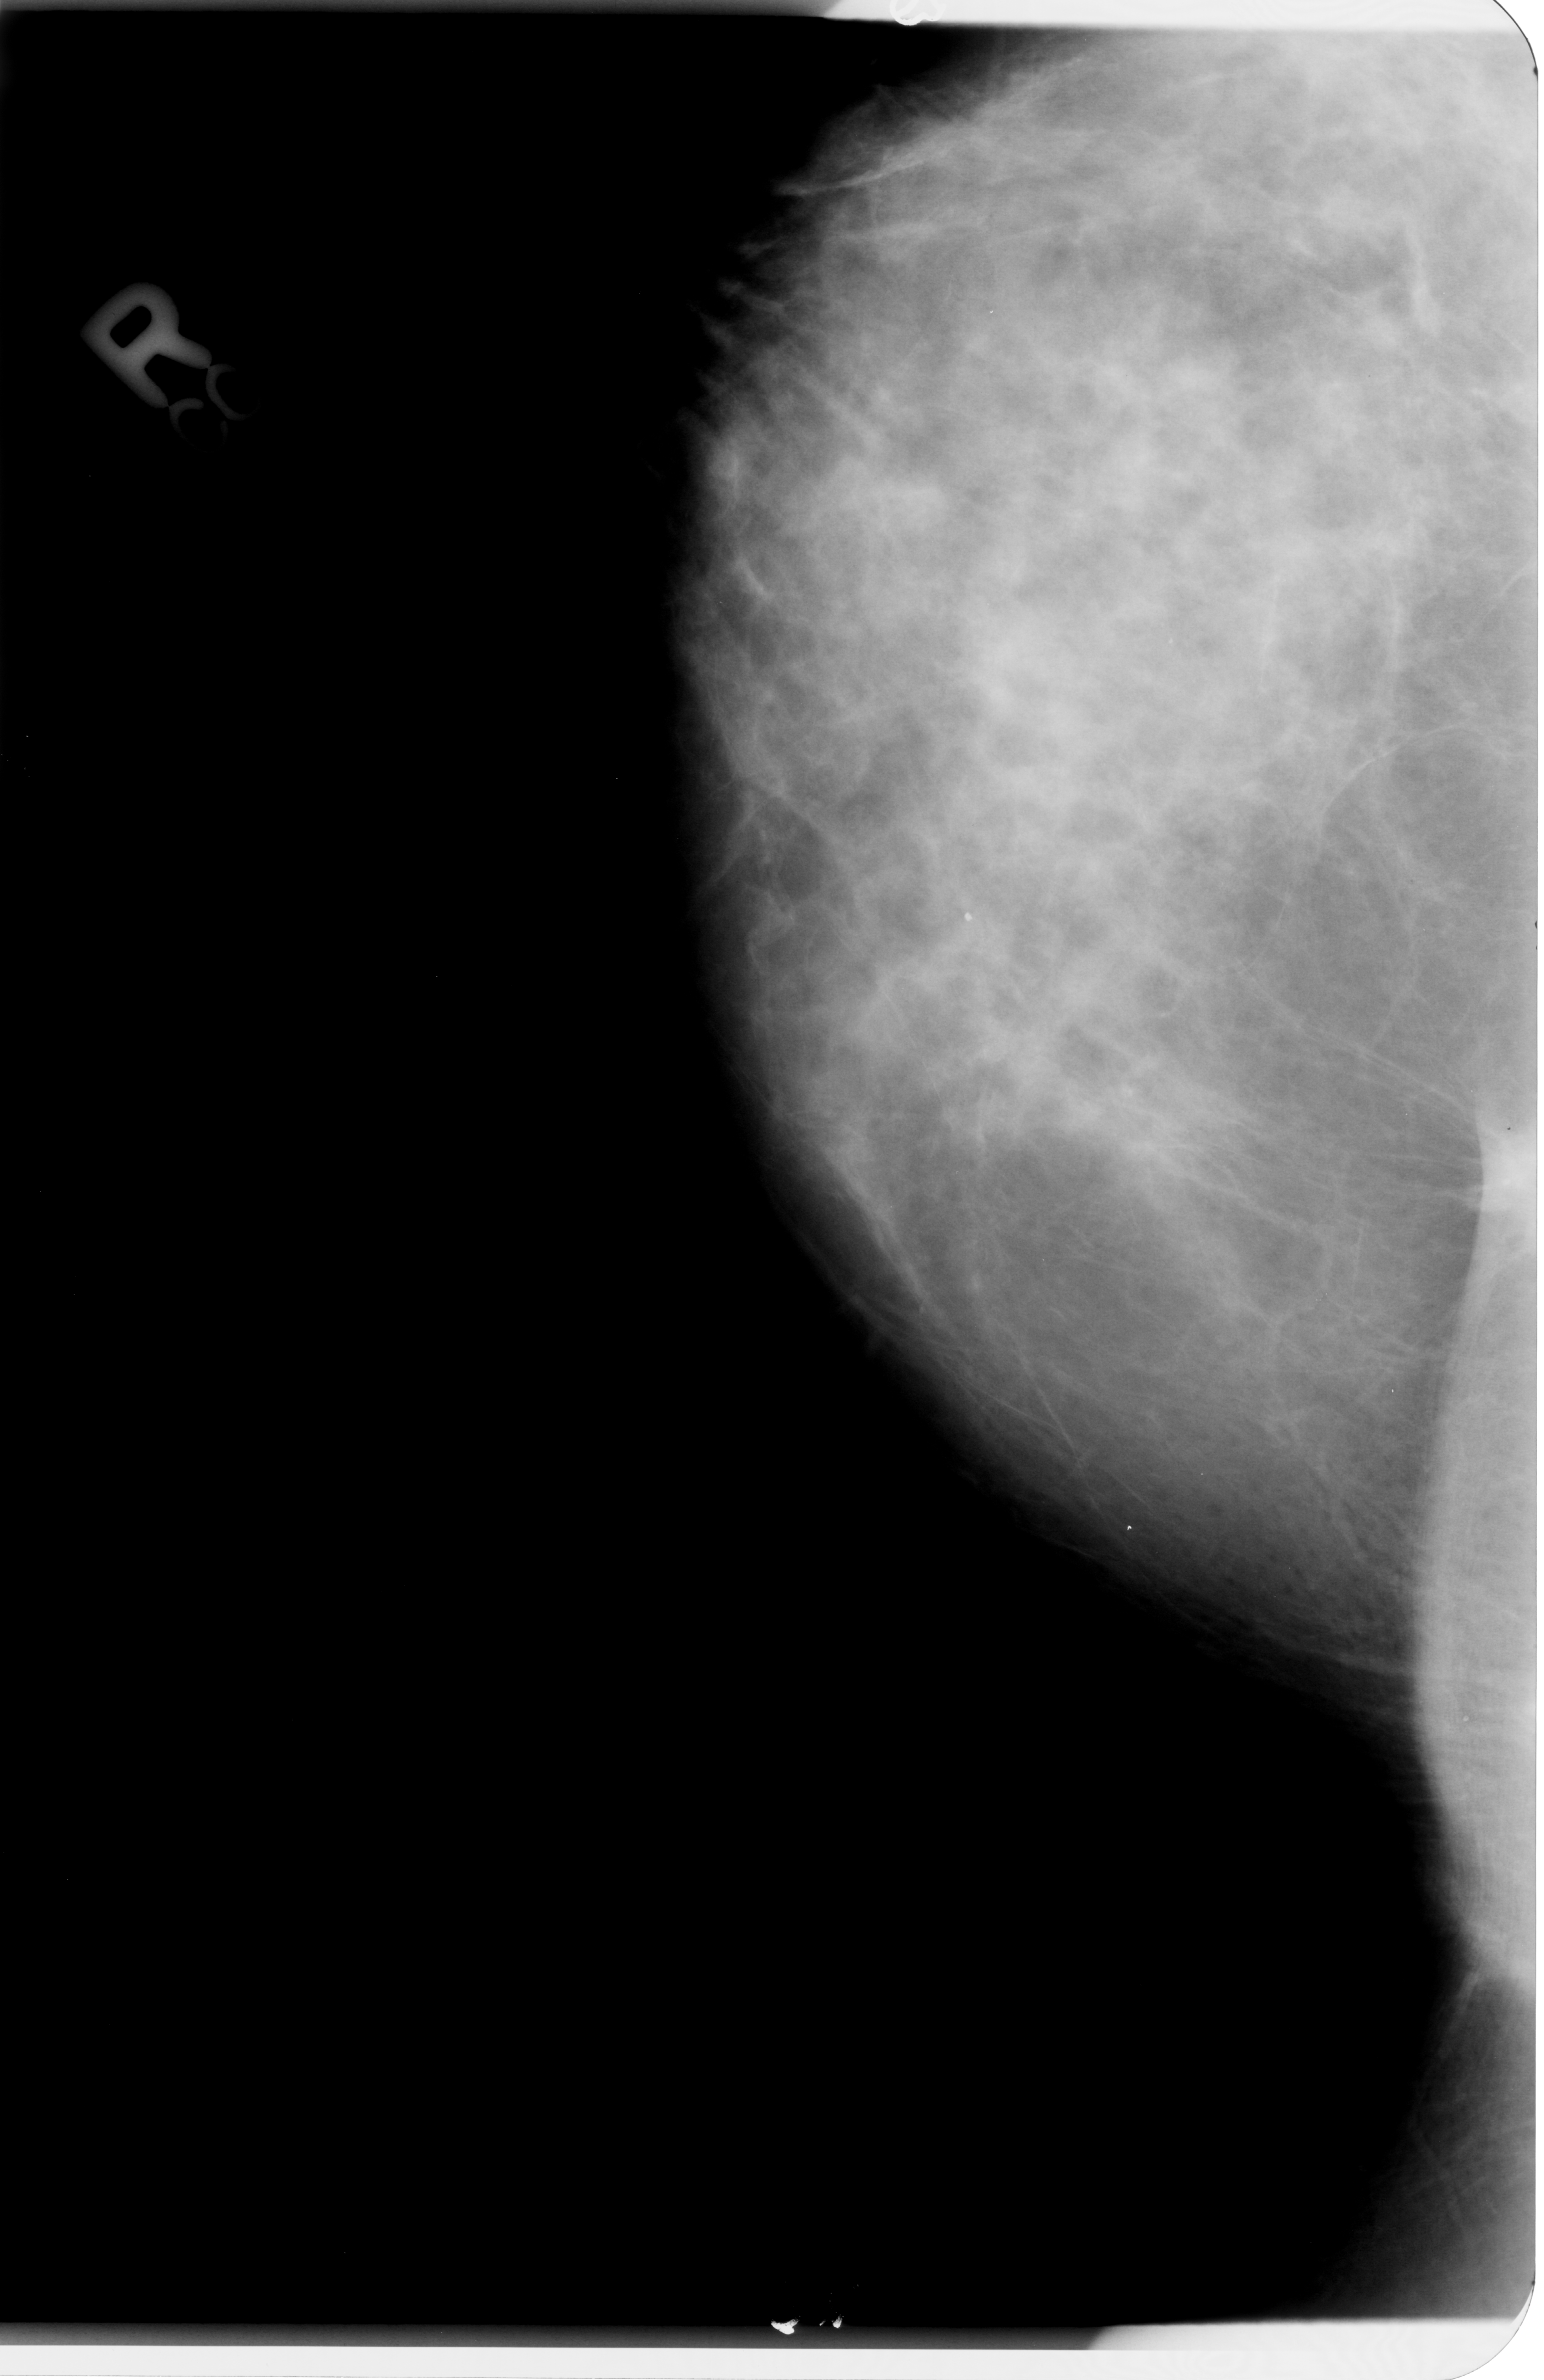
Mammogram (digitized film). Right breast. CC view. BI-RADS breast density category 3 (scale 1–4). 1544 × 2380 image matrix.
Expert-marked regions of interest on this film, with their recorded descriptors:
- mass, shape irregular, margins spiculated; BI-RADS assessment category 4; subtlety rating 4 on a 1 (subtle) to 5 (obvious) scale; pathology (as recorded): malignant: box from (x=1458, y=1113) to (x=1544, y=1229) px